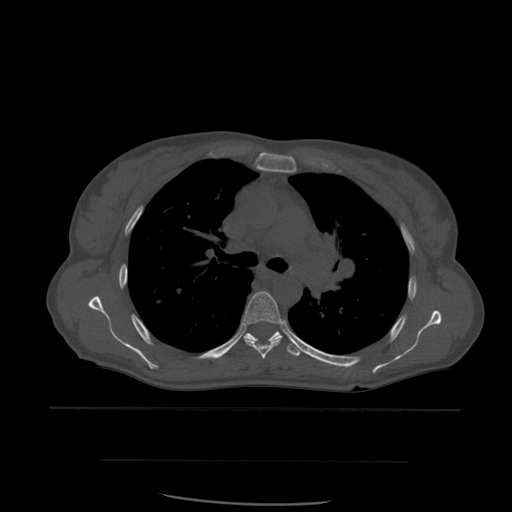
CT including the spine, one axial slice; slice 404 of 574 in the series (ordered by position); bone window (W 1800 / L 400 HU); 1.25 mm slice thickness; 512 × 512 image matrix, field of view 392 × 392 mm. Patient age 48 years. Case-level facts recorded for this patient, not image findings: primary cancer: lung; vertebrae with lytic lesions (as recorded): T11.
Annotated regions visible in this slice (semi-automatic segmentation, software-assisted and operator-edited):
- T5 vertebra: box from (x=243, y=291) to (x=285, y=359) px
- T6 vertebra: (x=227, y=331)–(x=301, y=357)